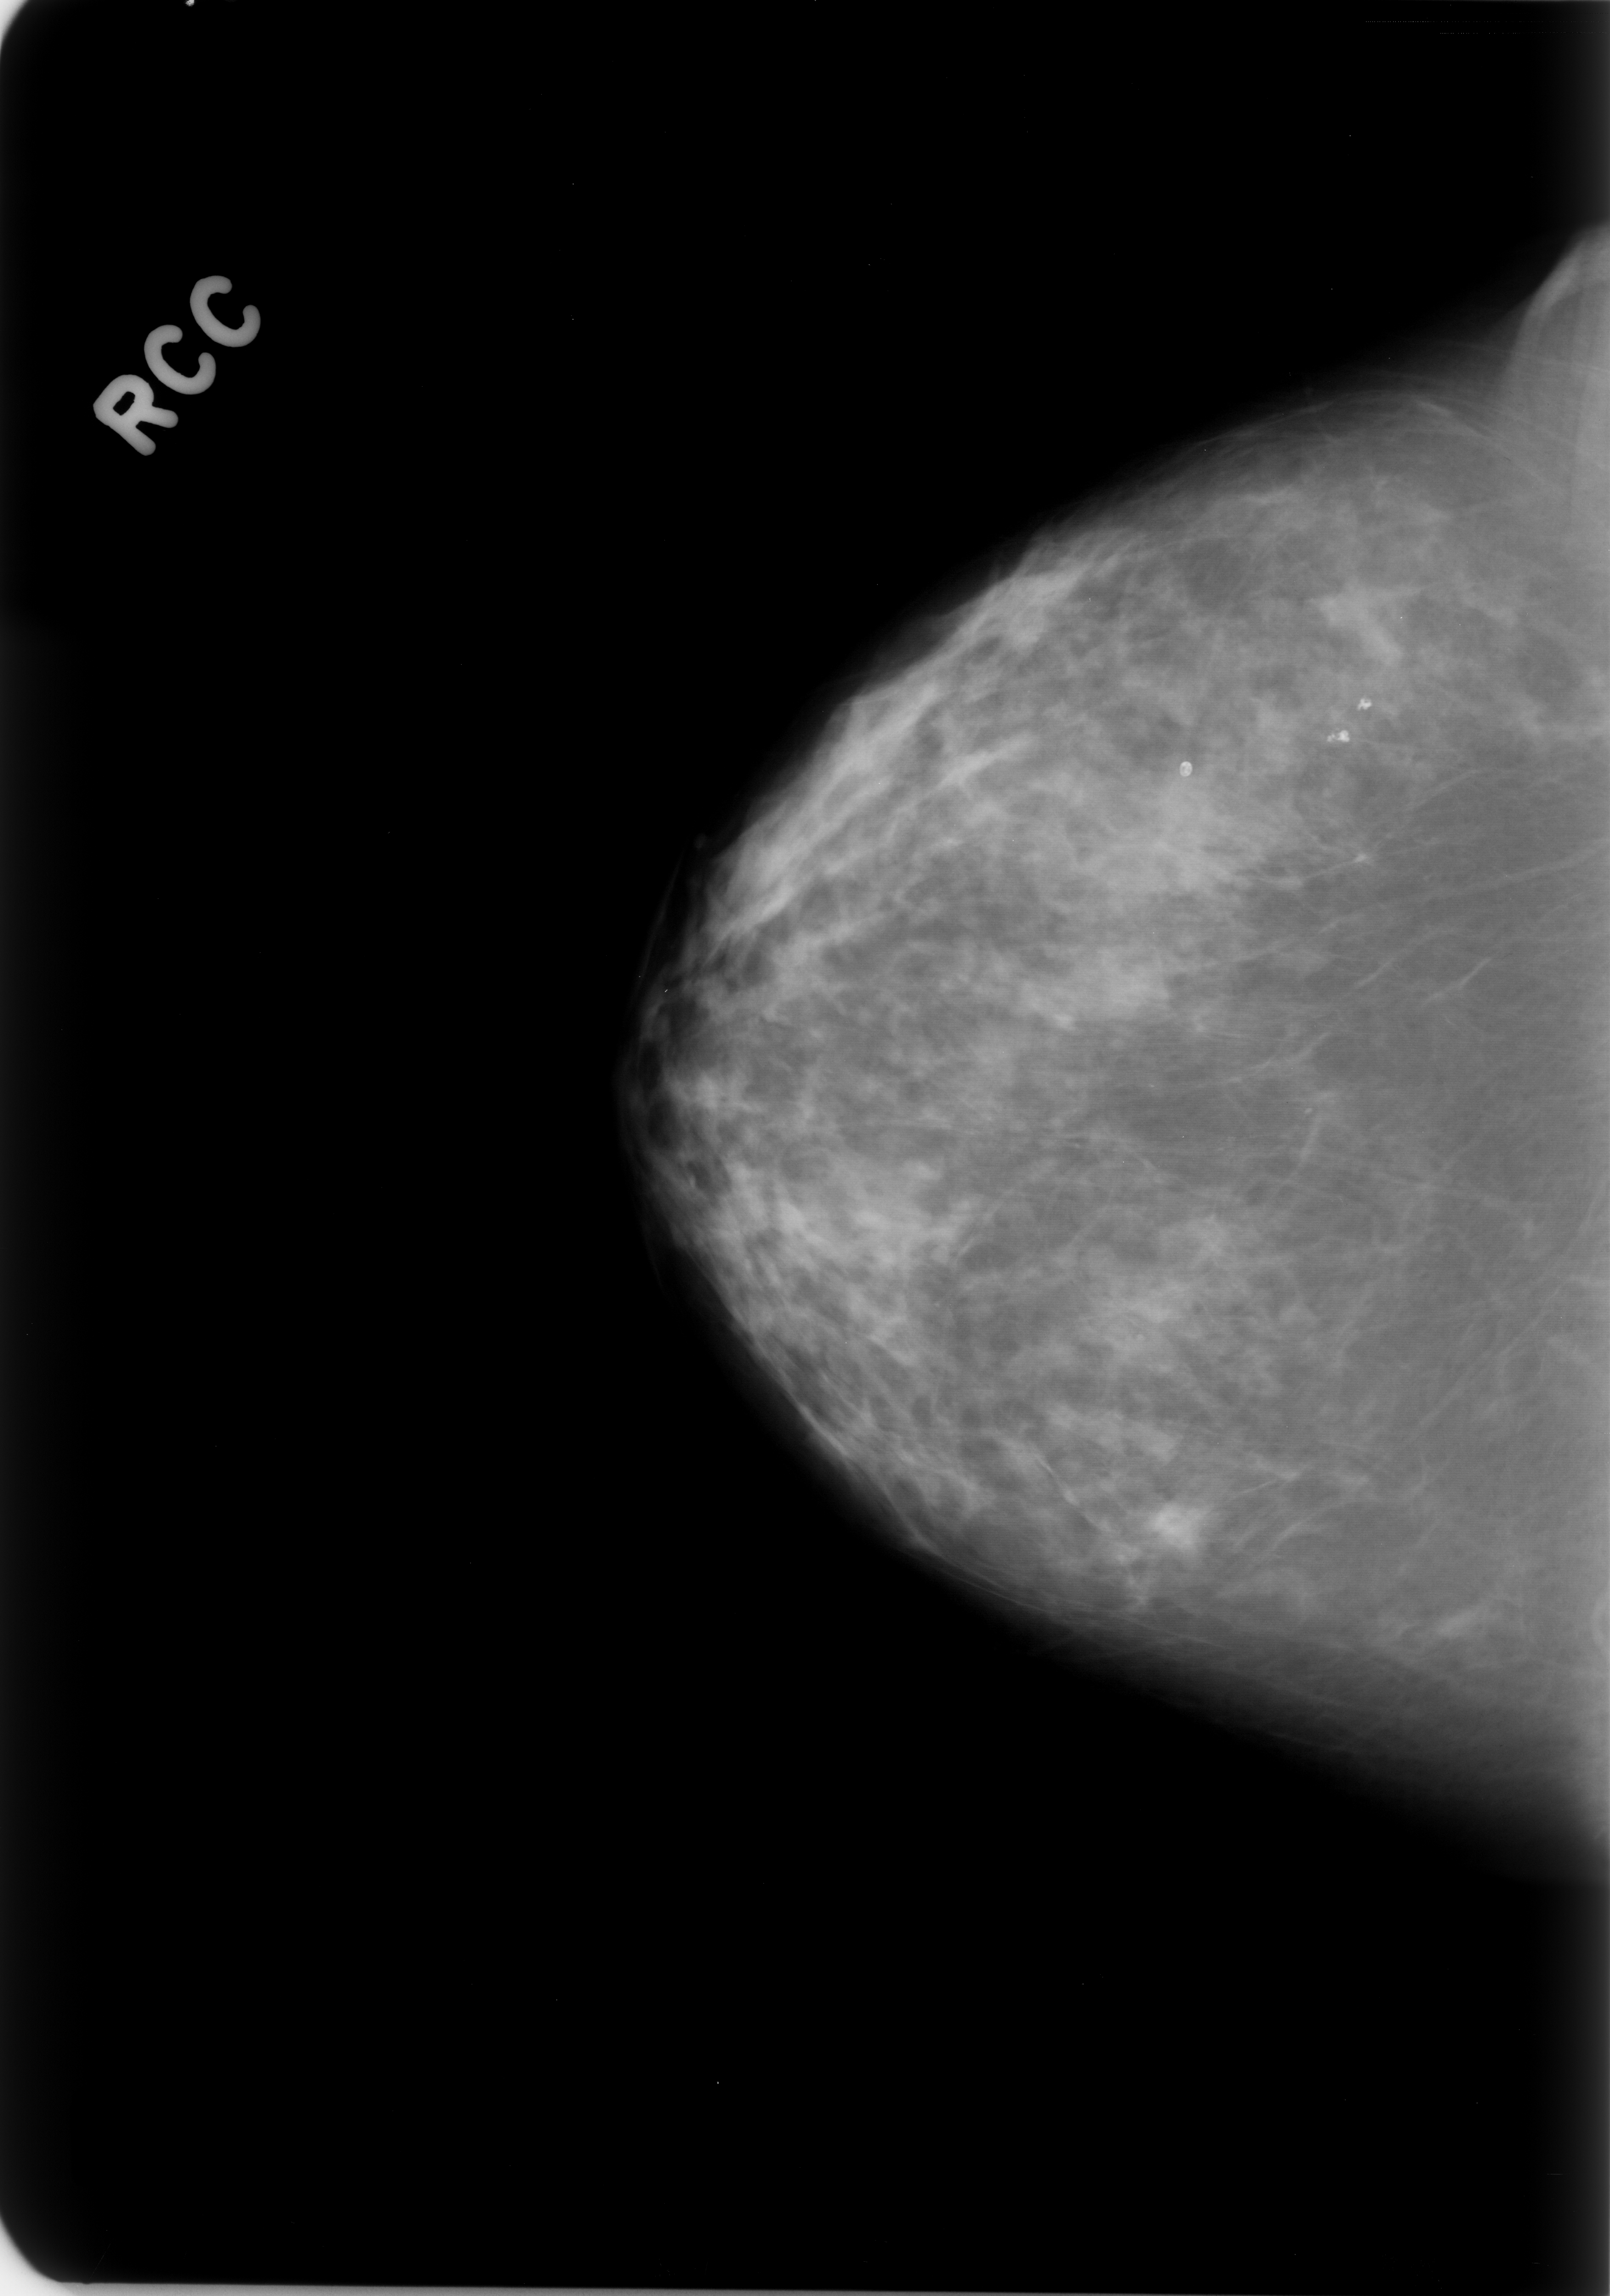
Digitized screen-film mammogram; right breast; craniocaudal (CC) view; breast composition: scattered fibroglandular densities (BI-RADS density category 2 of 4).
Calcifications, morphology fine linear branching, distribution linear; BI-RADS assessment category 4; subtlety rating 2 on a 1 (subtle) to 5 (obvious) scale; pathology result (as recorded, not read from the image): benign.